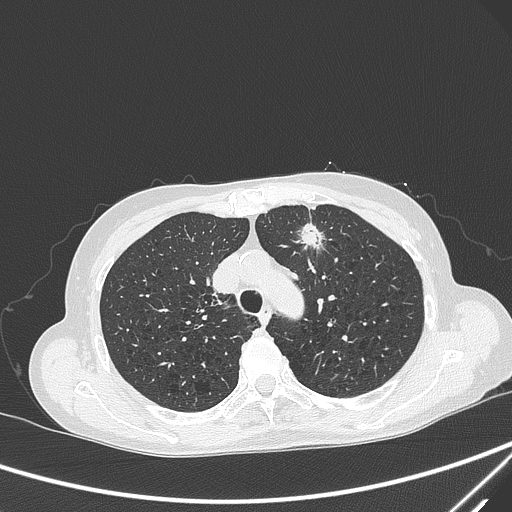
Chest CT, one axial slice. Position 226 of 299 along the scan axis. 120 kVp. Lung window (W 1500 / L -600 HU). 1 mm slice thickness. 512 × 512 image matrix, field of view 350 × 350 mm. Female patient, age 71 years. From the clinical record (not read from this slice): clinical TNM (as recorded): T1c N0 M0.
Structures marked on this image (bounding box drawn by a radiologist):
- lung tumour (recorded histology: adenocarcinoma): box from (x=291, y=215) to (x=329, y=263) px